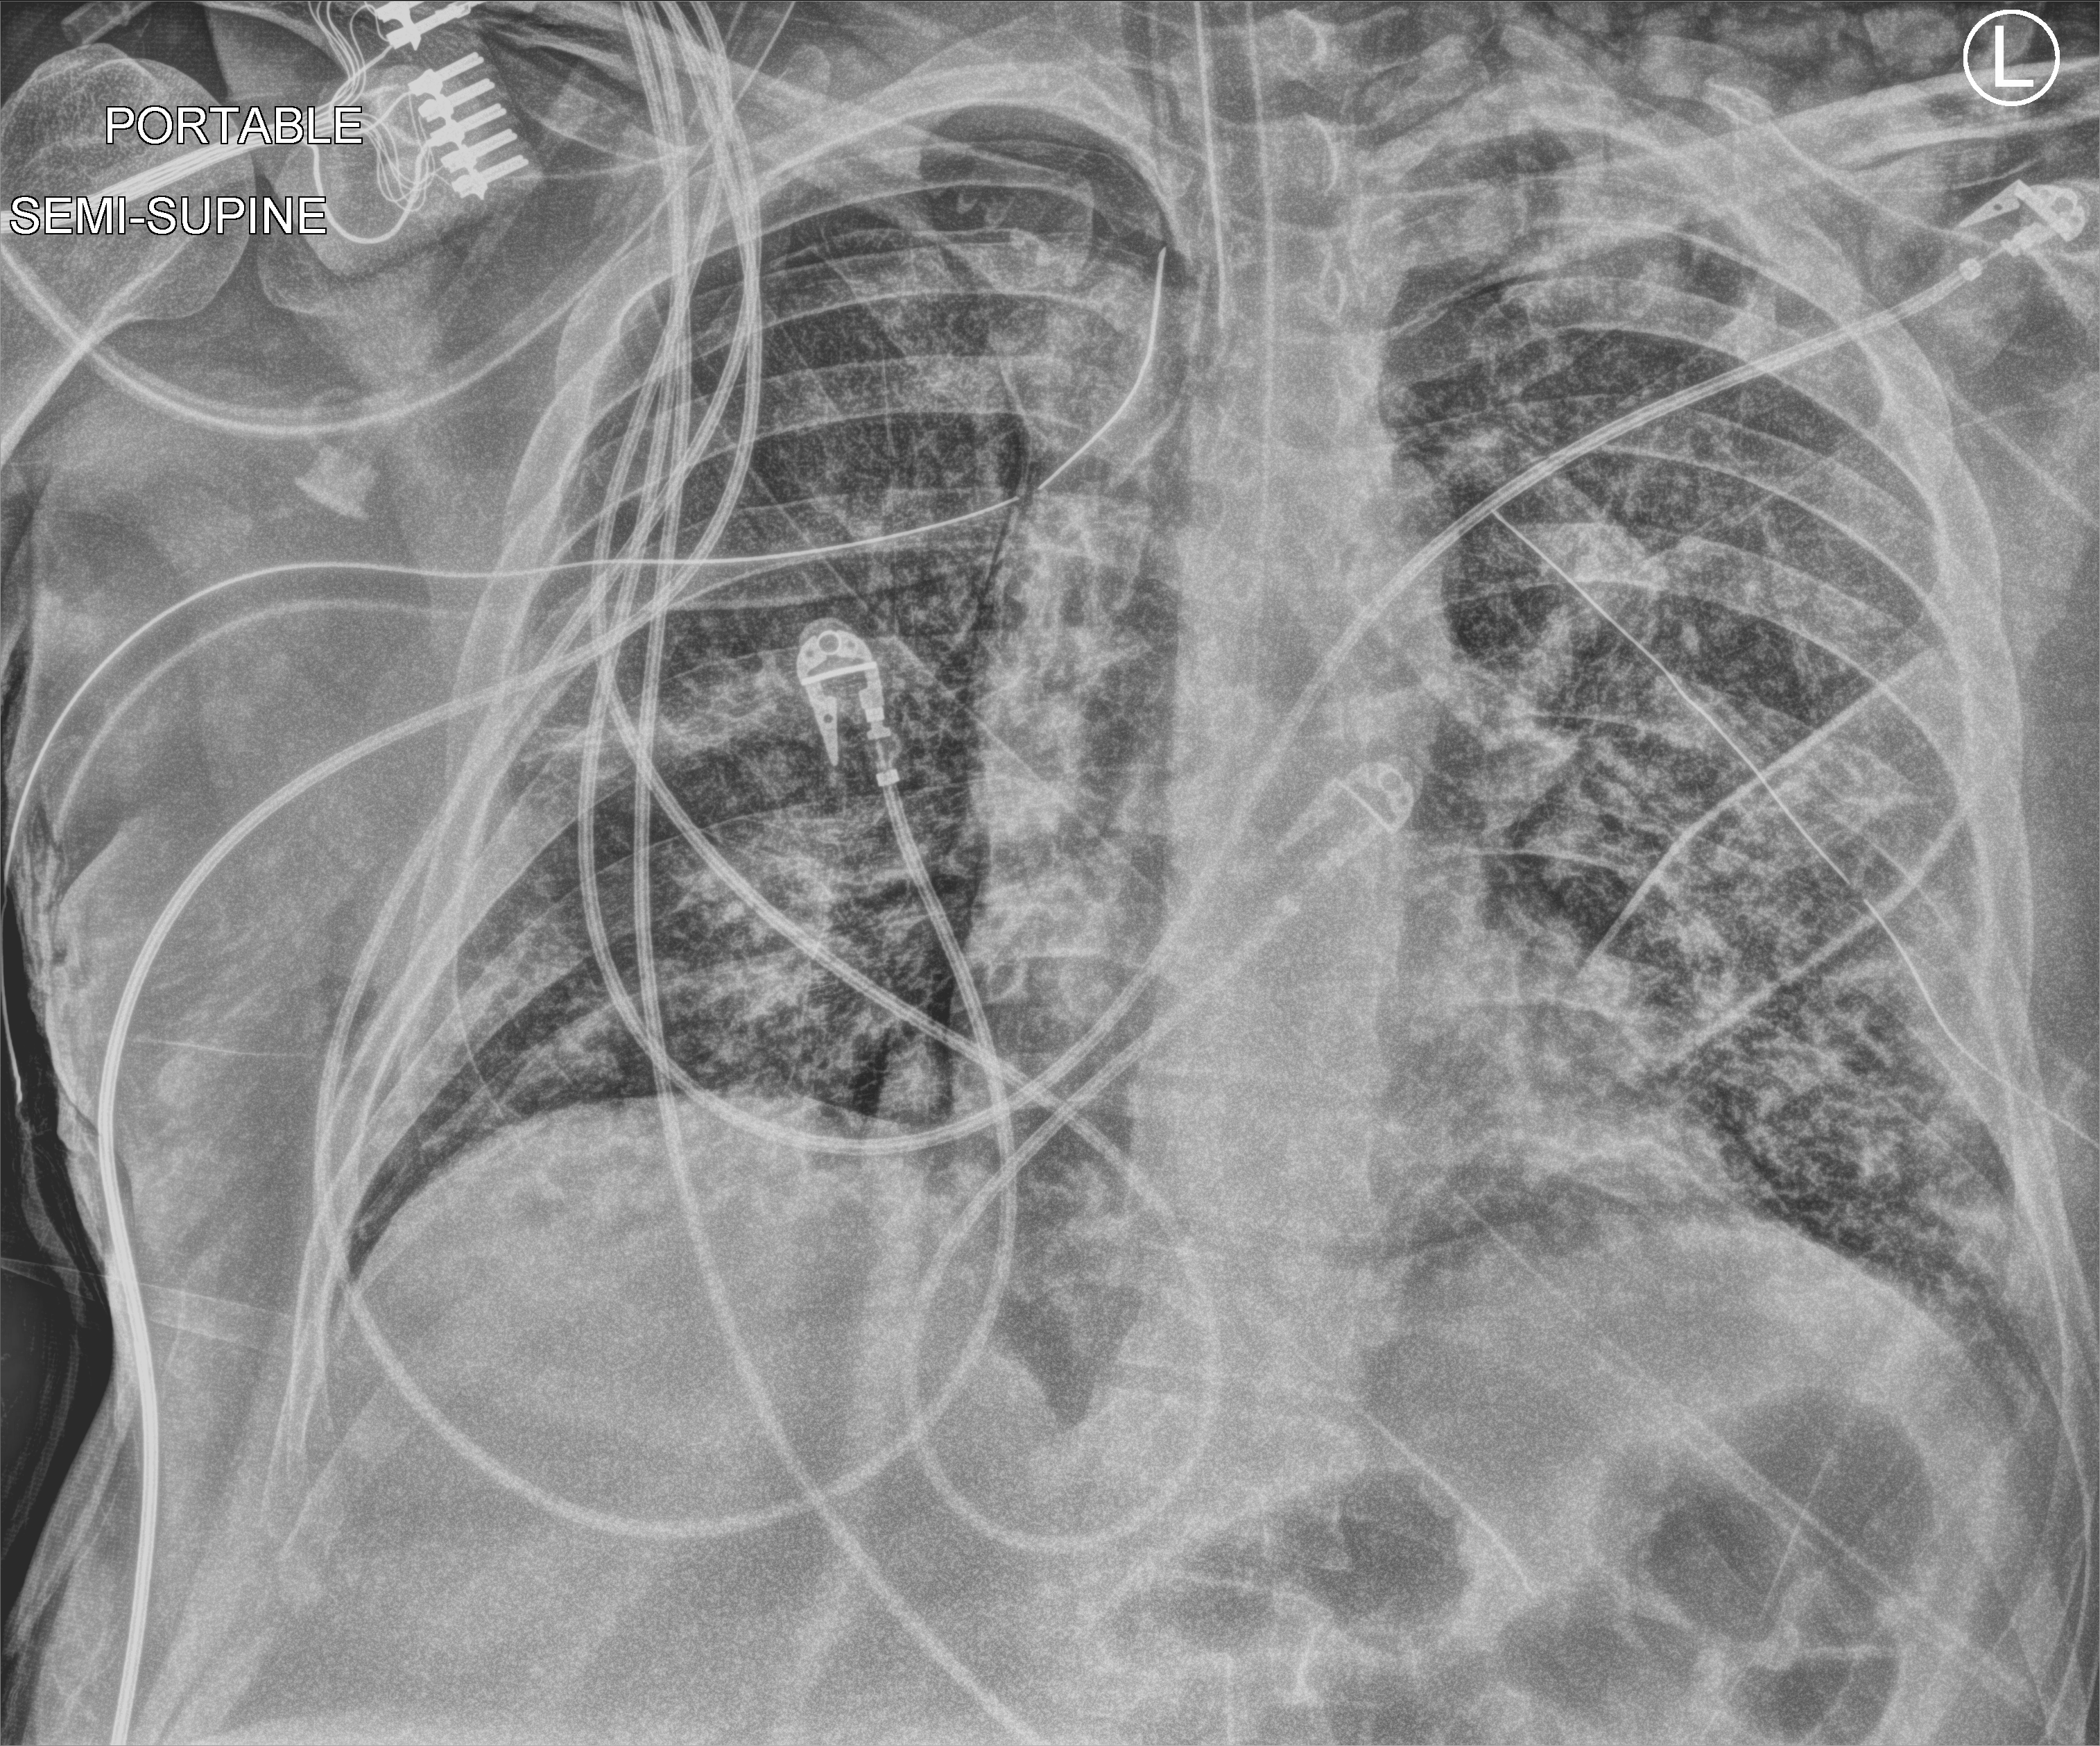
Portable chest radiograph, anteroposterior (AP) projection. Male patient hospitalised with COVID-19, age 18–59 years.
Admission-level facts for this patient (not findings on this image; timing relative to this image not recorded):
- admitted to intensive care during this hospital stay: yes